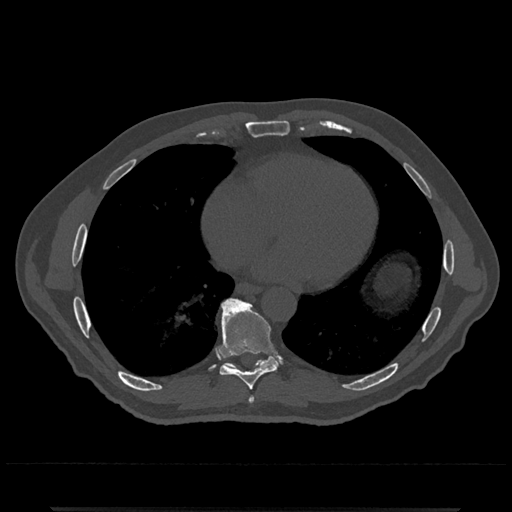
CT including the spine, one axial slice. Slice 656 of 797 in the series (ordered by position). 120 kVp. Bone window (W 1800 / L 400 HU). 0.5 mm slice thickness. 512 × 512 image matrix. Male patient, age 67 years. Case-level facts recorded for this patient, not image findings: primary cancer: prostate.
Structures marked on this image (semi-automatically segmented with operator editing):
- T7 vertebra: bounding box [x1, y1, x2, y2] px = [248, 396, 254, 403]
- T8 vertebra: [217, 297, 282, 390]
- T9 vertebra: [219, 299, 278, 369]